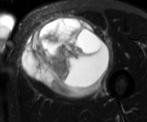
MRI of an extremity soft-tissue mass, one axial slice. Position 36 of 52 along the scan axis. T2-weighted fat-saturated. MR volume resampled by the dataset authors to the PET/CT grid (not the native acquisition matrix). 147 × 122 image matrix. Male patient. Case-level facts recorded for this patient, not image findings: histological type: pleiomorphic liposarcoma; grade: high; site of the primary tumour: left thigh.
Annotated regions visible in this slice (expert contour drawn on MRI and transferred to this co-registered scan by the dataset authors):
- gross tumour volume including surrounding oedema: bounding box [x1, y1, x2, y2] px = [23, 16, 111, 95]
- gross tumour volume (mass): [23, 16, 108, 95]